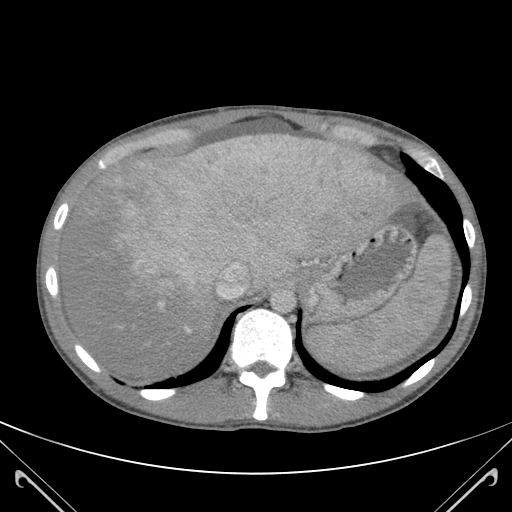
Contrast-enhanced abdominal CT (liver protocol), one axial slice. Position 94 of 118 along the scan axis. Soft-tissue window (W 400 / L 40 HU). 3 mm slice thickness. 512 × 512 image matrix, field of view 380 × 380 mm. Case-level facts recorded for this patient, not image findings: diagnosis: hepatocellular carcinoma (patient treated with transarterial chemoembolisation; whether this scan precedes or follows treatment is not stated here); TNM stage (as recorded): Stage-IIIB; Child-Pugh class: A.
Outlined on this slice (semi-automatically segmented with operator editing):
- abdominal aorta: bounding box (x1, y1, x2, y2) in pixels: (273, 289, 295, 312)
- liver parenchyma outside the tumour (the mass and vessels are separate outlines, so this box may not span the whole liver): (62, 133, 422, 377)
- mass: (100, 135, 377, 302)
- liver vessels: (158, 140, 385, 332)